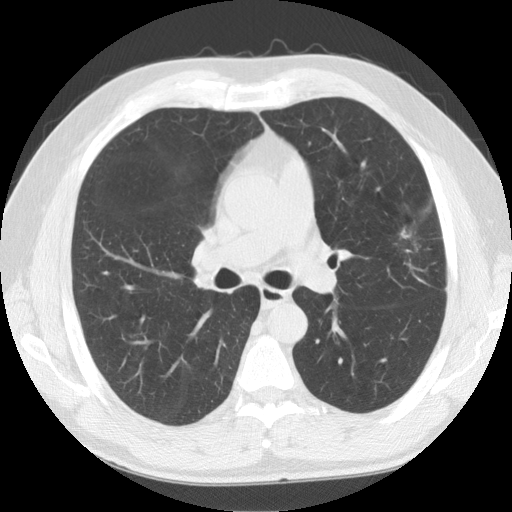
Low-dose screening chest CT, one axial slice. Position 89 of 141 along the scan axis. 120 kVp. Lung window (W 1500 / L -600 HU). 2.5 mm slice thickness. 512 × 512 image matrix, field of view 360 × 360 mm.
Structures marked on this image (outlined manually by an expert reader):
- lesion 1 (tumor, upper lobe of left lung): bounding box (x1, y1, x2, y2) in pixels: (401, 230, 410, 239)